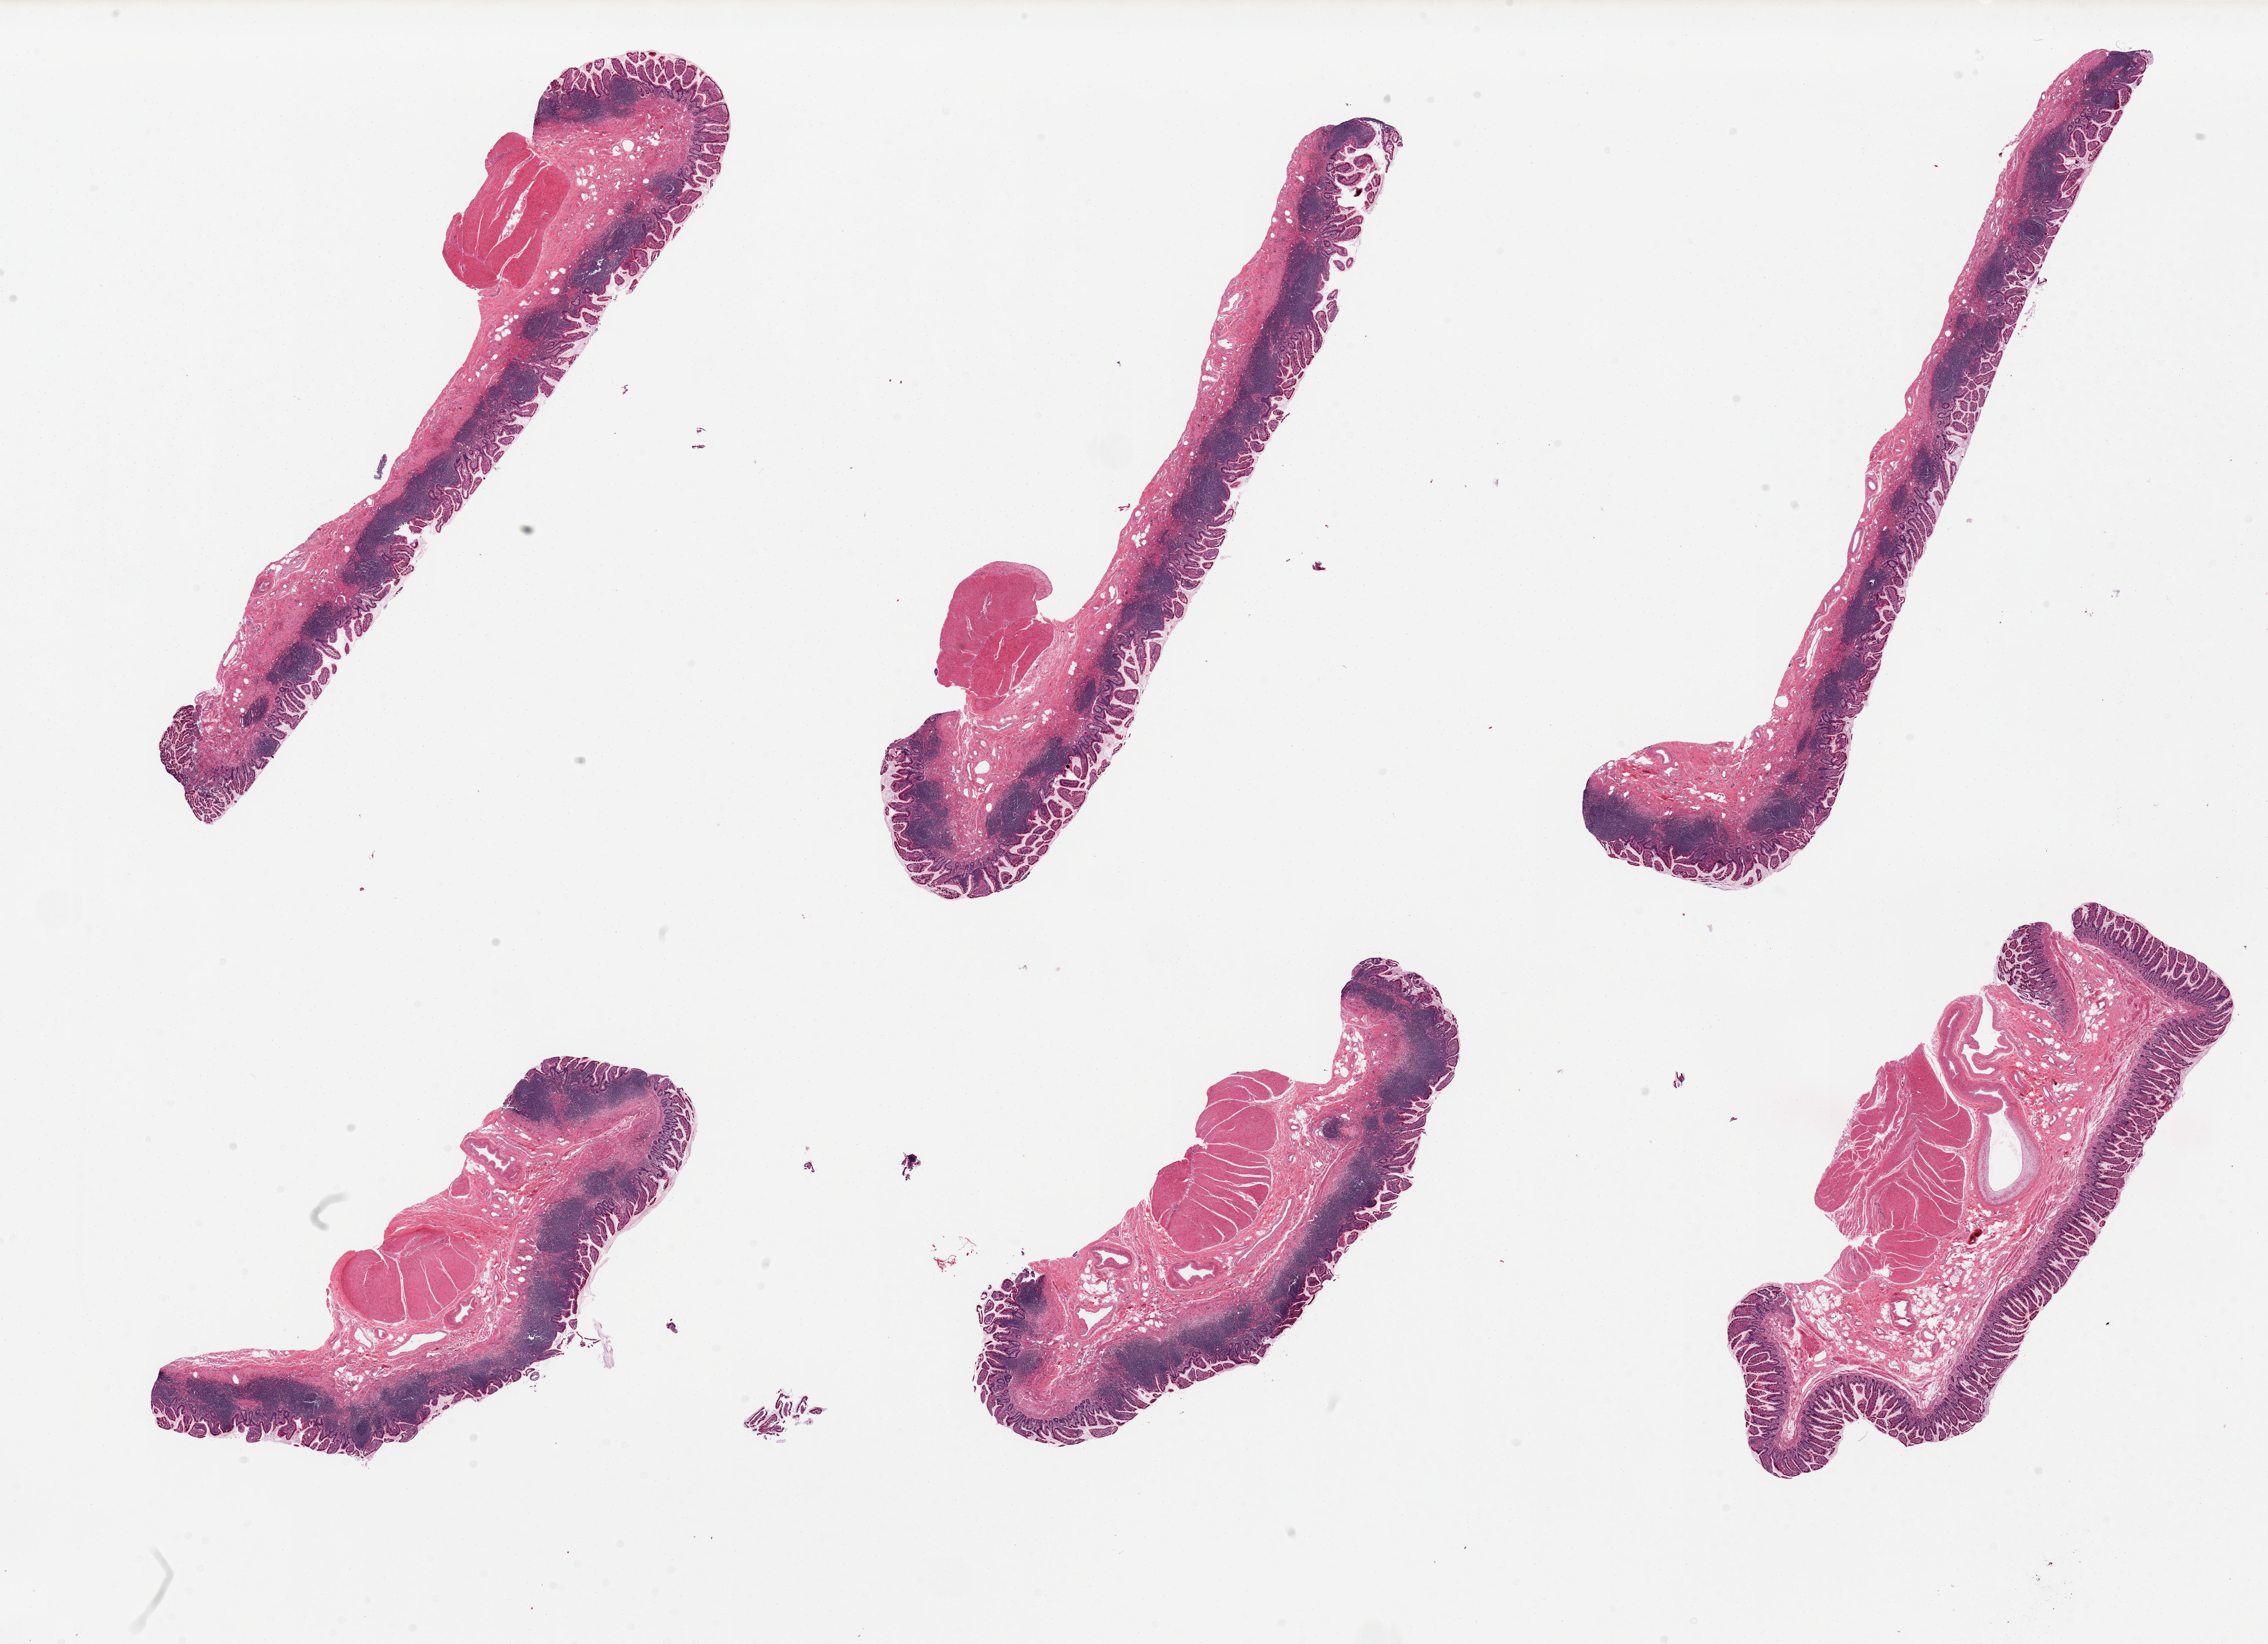
Whole-slide image, H&E stain, whole scanned area (about 30.5 x 22.1 mm, acquisition: 20x scan) shown as a low-resolution overview, PAXgene-fixed paraffin-embedded (PFPE) section, sampled site (target tissue): ileum, tissue donor sample. Male donor.
* pathologist's review note for this sample: 6 pieces; abundant lymphoid tissue in 5 of 6 pieces